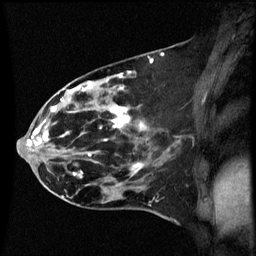
Breast MRI (dynamic contrast-enhanced), one sagittal slice; slice 28 of 60 in the series (ordered by position); dynamic contrast-enhanced series, image 2 of 3 at this slice position (ordered by acquisition); 1.5 T; TE 4.2 ms, TR 8.9 ms; 256 × 256 image matrix. Patient: female, 44 years. Case-level facts recorded for this patient, not image findings: setting: breast cancer imaged before/during neoadjuvant chemotherapy; receptor status: HR-positive, HER2-negative.
Annotated regions visible in this slice (semi-automatic segmentation, software-assisted and operator-edited):
- analysis volume of interest (the breast-tissue region the enhancement analysis was run in; not a lesion): bounding box (x1, y1, x2, y2) in pixels: (43, 78, 153, 189)
- tumour enhancement mask (voxels above the 70 % enhancement threshold inside the analysis volume of interest): (52, 84, 146, 177)